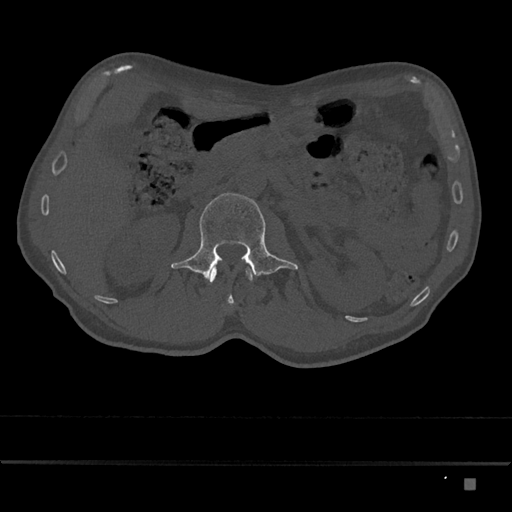
CT including the spine, one axial slice. Position 493 of 797 along the scan axis. Reconstruction kernel Br40s/3. 120 kVp. Bone window (W 1800 / L 400 HU). 0.5 mm slice thickness. 512 × 512 image matrix, field of view 390 × 390 mm. Male patient, age 72 years. From the clinical record (not read from this slice): primary cancer: prostate.
Structures marked on this image (semi-automatically segmented with operator editing):
- L1 vertebra: bounding box (x1, y1, x2, y2) in pixels: (210, 266, 253, 305)
- L2 vertebra: (171, 193, 298, 281)